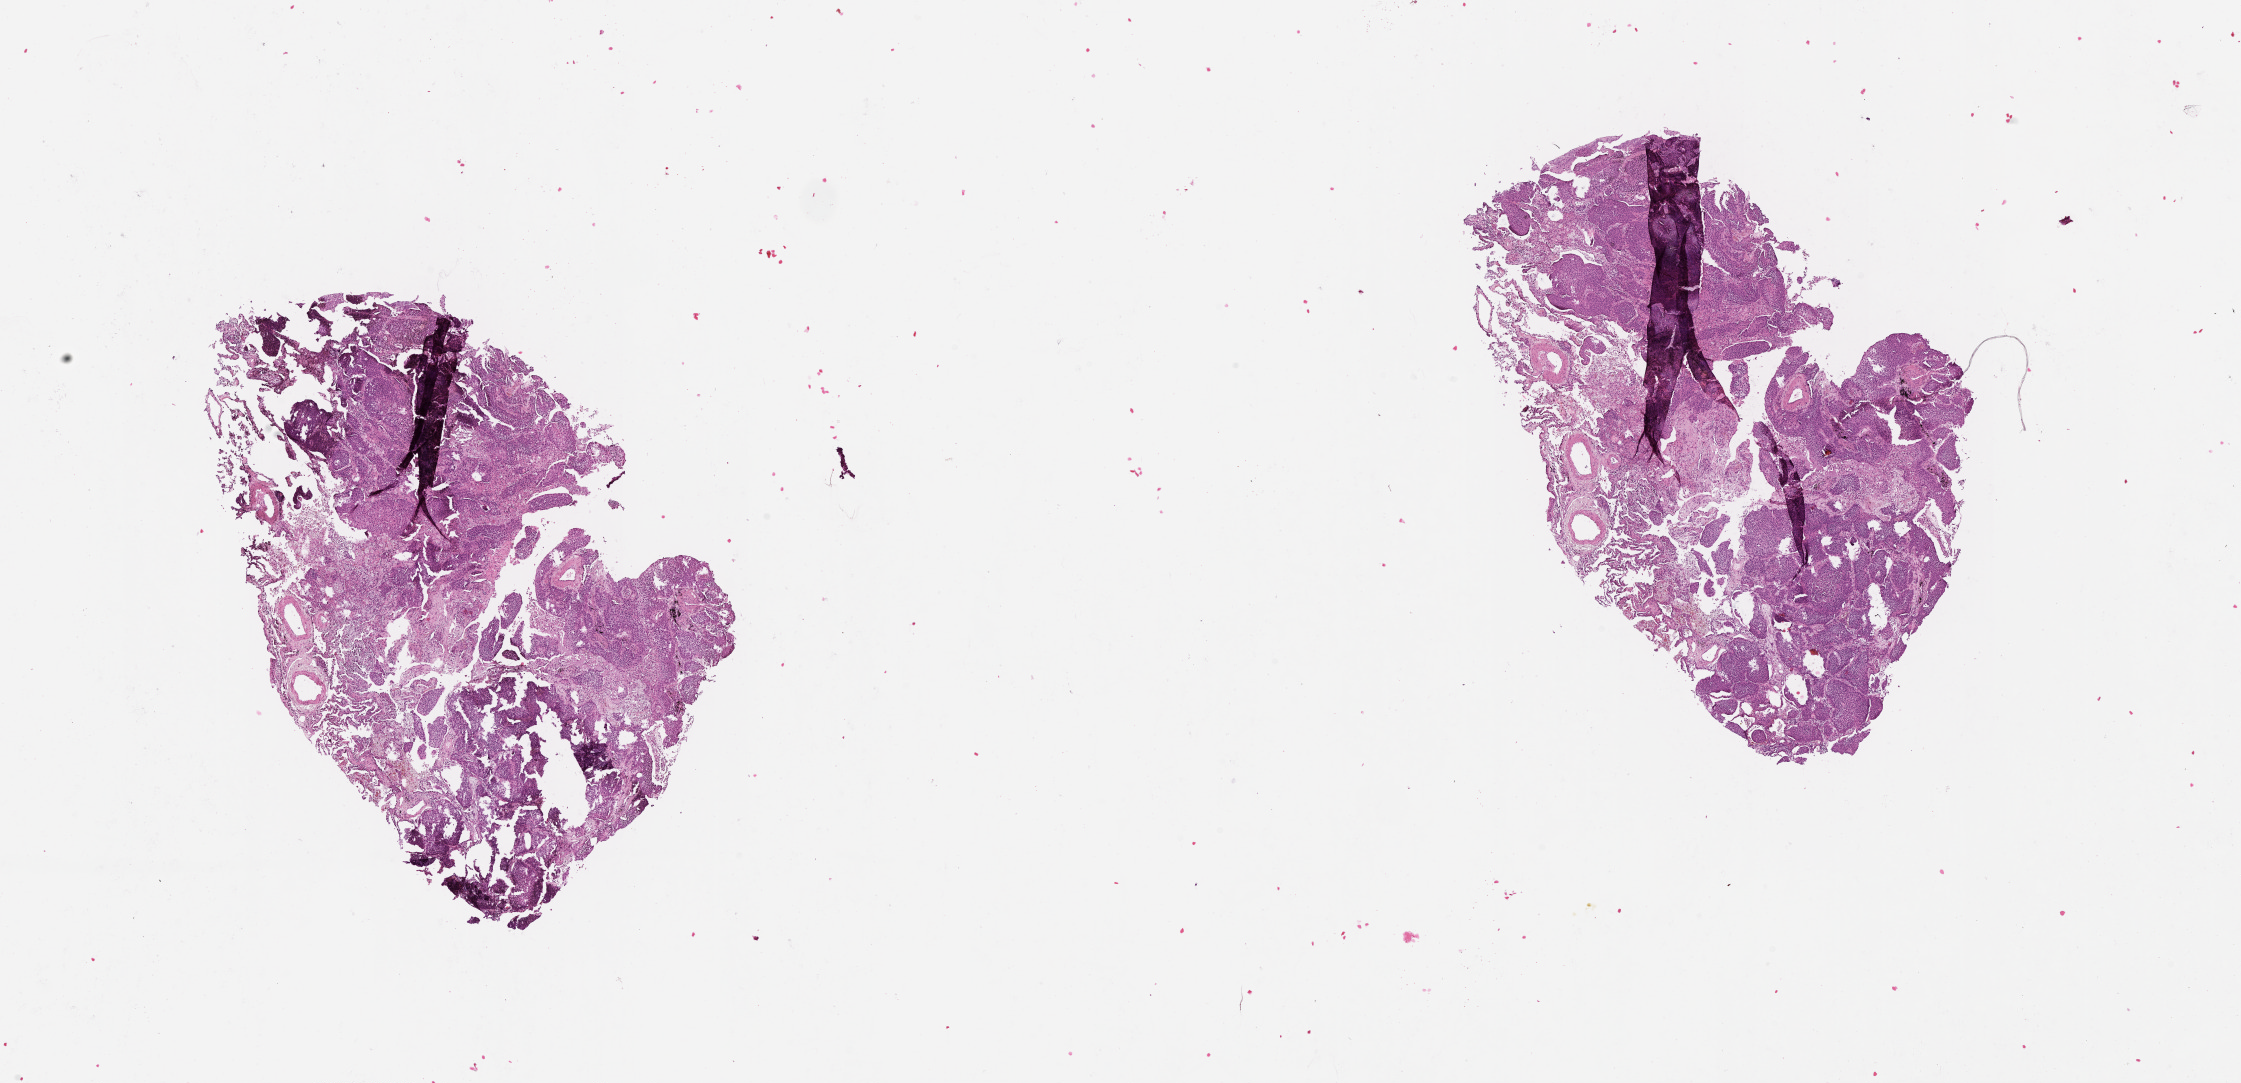
Whole-slide histology image, H&E-stained, a low-resolution overview of the entire scanned area, about 18.0 x 8.7 mm (slide scanned at 20x); tumour tissue sample, lung. Patient: male, age 64 years.
* patient diagnosis (cohort enrolment): squamous cell carcinoma (lung)